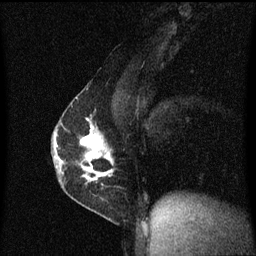
Breast MRI (dynamic contrast-enhanced), one sagittal slice; slice 35 of 60 in the series (ordered by position); dynamic contrast-enhanced series, image 2 of 3 at this slice position (ordered by acquisition); 1.5 T; TE 4.2 ms, TR 8.4 ms; 256 × 256 image matrix, field of view 200 × 200 mm. Female patient, age 40 years.
Structures marked on this image (semi-automatic segmentation, software-assisted and operator-edited):
- analysis volume of interest (the breast-tissue region the enhancement analysis was run in; not a lesion): box from (x=57, y=110) to (x=114, y=191) px
- tumour enhancement mask (voxels above the 70 % enhancement threshold inside the analysis volume of interest): (x=57, y=118)–(x=113, y=183)